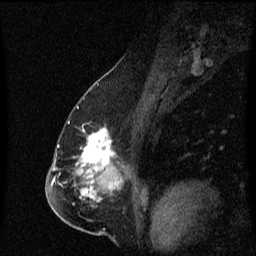
Breast MRI (dynamic contrast-enhanced), one sagittal slice. Position 36 of 60 along the scan axis. Dynamic contrast-enhanced series, image 2 of 3 at this slice position (ordered by acquisition). 1.5 T. TE 4.2 ms, TR 8.4 ms. 256 × 256 image matrix. Female patient, age 57 years. Case-level facts recorded for this patient, not image findings: setting: breast cancer imaged before/during neoadjuvant chemotherapy; receptor status: HR-positive, HER2-negative.
Structures marked on this image (semi-automatically segmented with operator editing):
- analysis volume of interest (the breast-tissue region the enhancement analysis was run in; not a lesion): bounding box (x1, y1, x2, y2) in pixels: (68, 118, 128, 177)
- tumour enhancement mask (voxels above the 70 % enhancement threshold inside the analysis volume of interest): (81, 130, 115, 171)